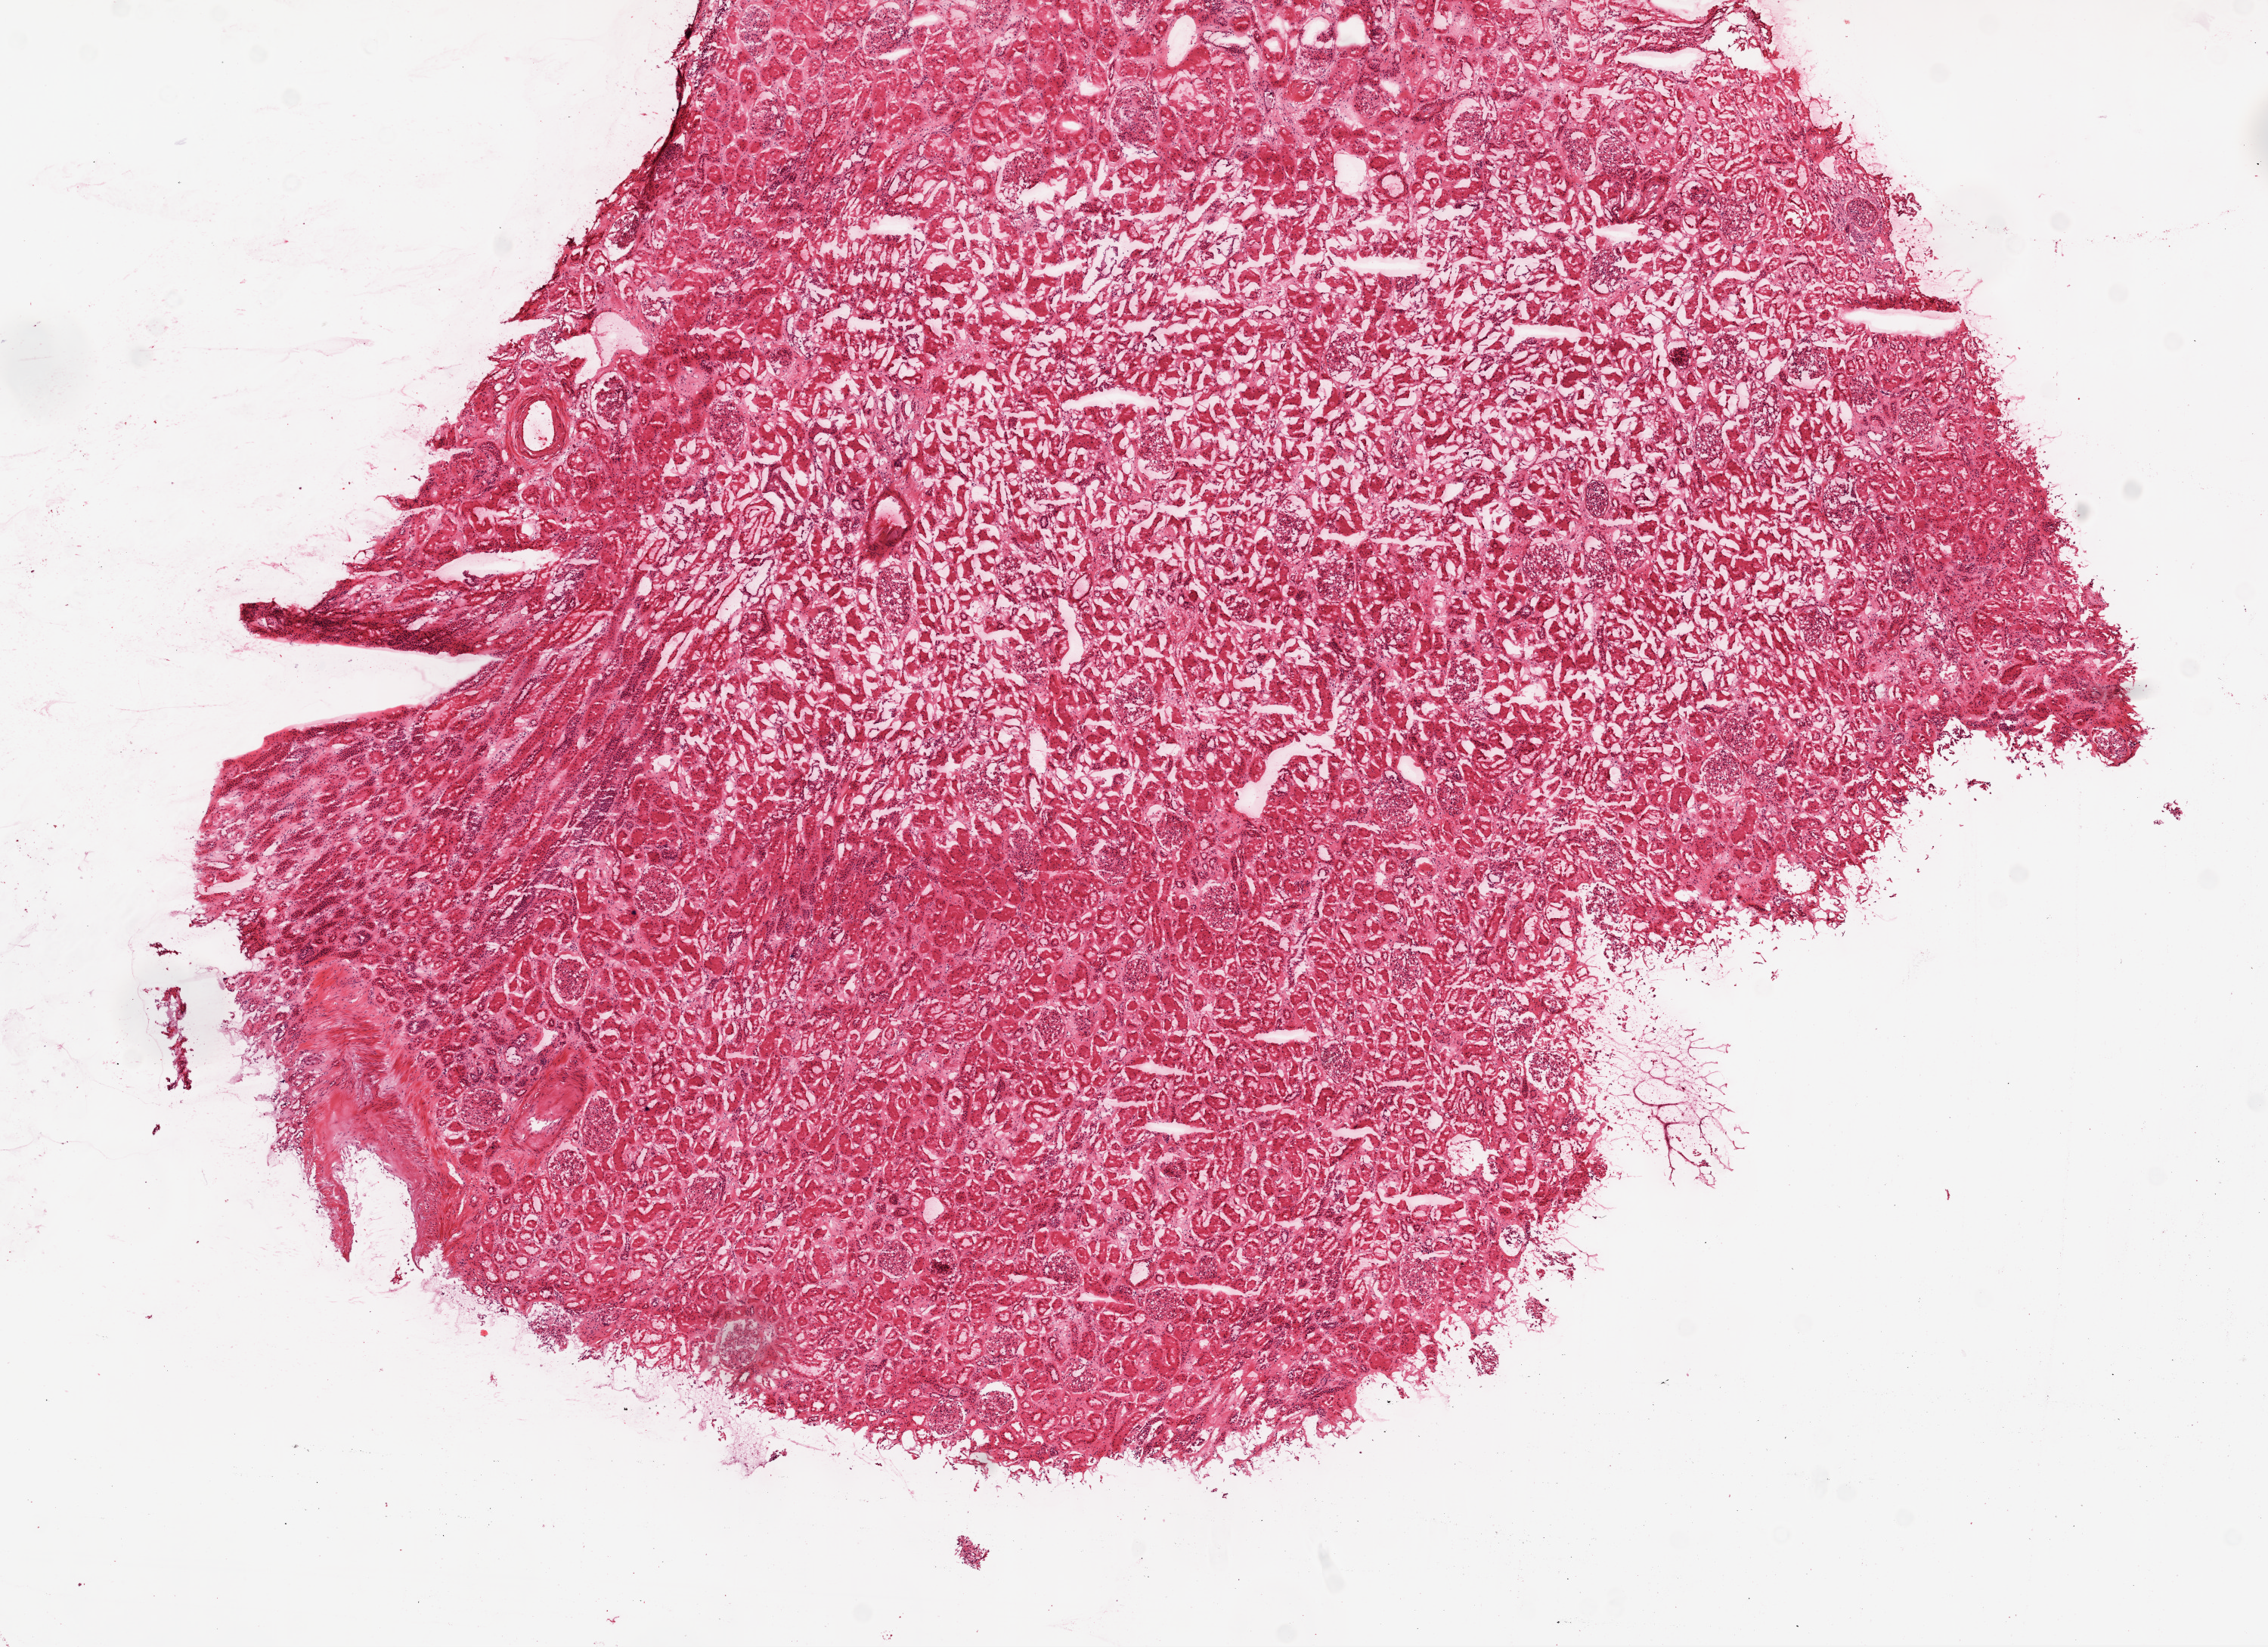
Whole-slide histology image, H&E — whole scanned area (about 12.0 x 8.7 mm) shown as a low-resolution overview. Frozen section from the top of the tissue portion. Solid tissue normal (non-tumour tissue) sample from the kidney. Male, age 63 years at initial diagnosis.
This section: solid tissue normal (non-tumour) sample from the same patient. Patient diagnosis: Clear cell adenocarcinoma, NOS.